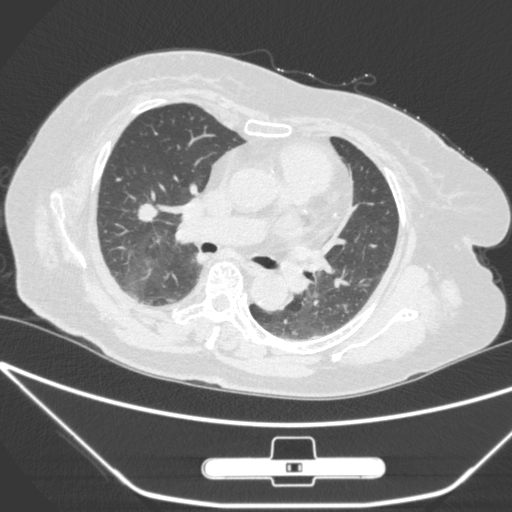
Chest CT, one axial slice. Slice 155 of 245 in the series (ordered by position). Lung window (W 1500 / L -600 HU). 512 × 512 image matrix, field of view 365 × 365 mm. Female patient, age 65 years. Case-level facts recorded for this patient, not image findings: clinical TNM (as recorded): T1c N0 M0; histopathological grade: G3.
Annotated regions visible in this slice (rectangle marked by the reading radiologist):
- lung tumour (recorded histology: adenocarcinoma): bounding box <131,195,163,231> (left, top, right, bottom; pixels)